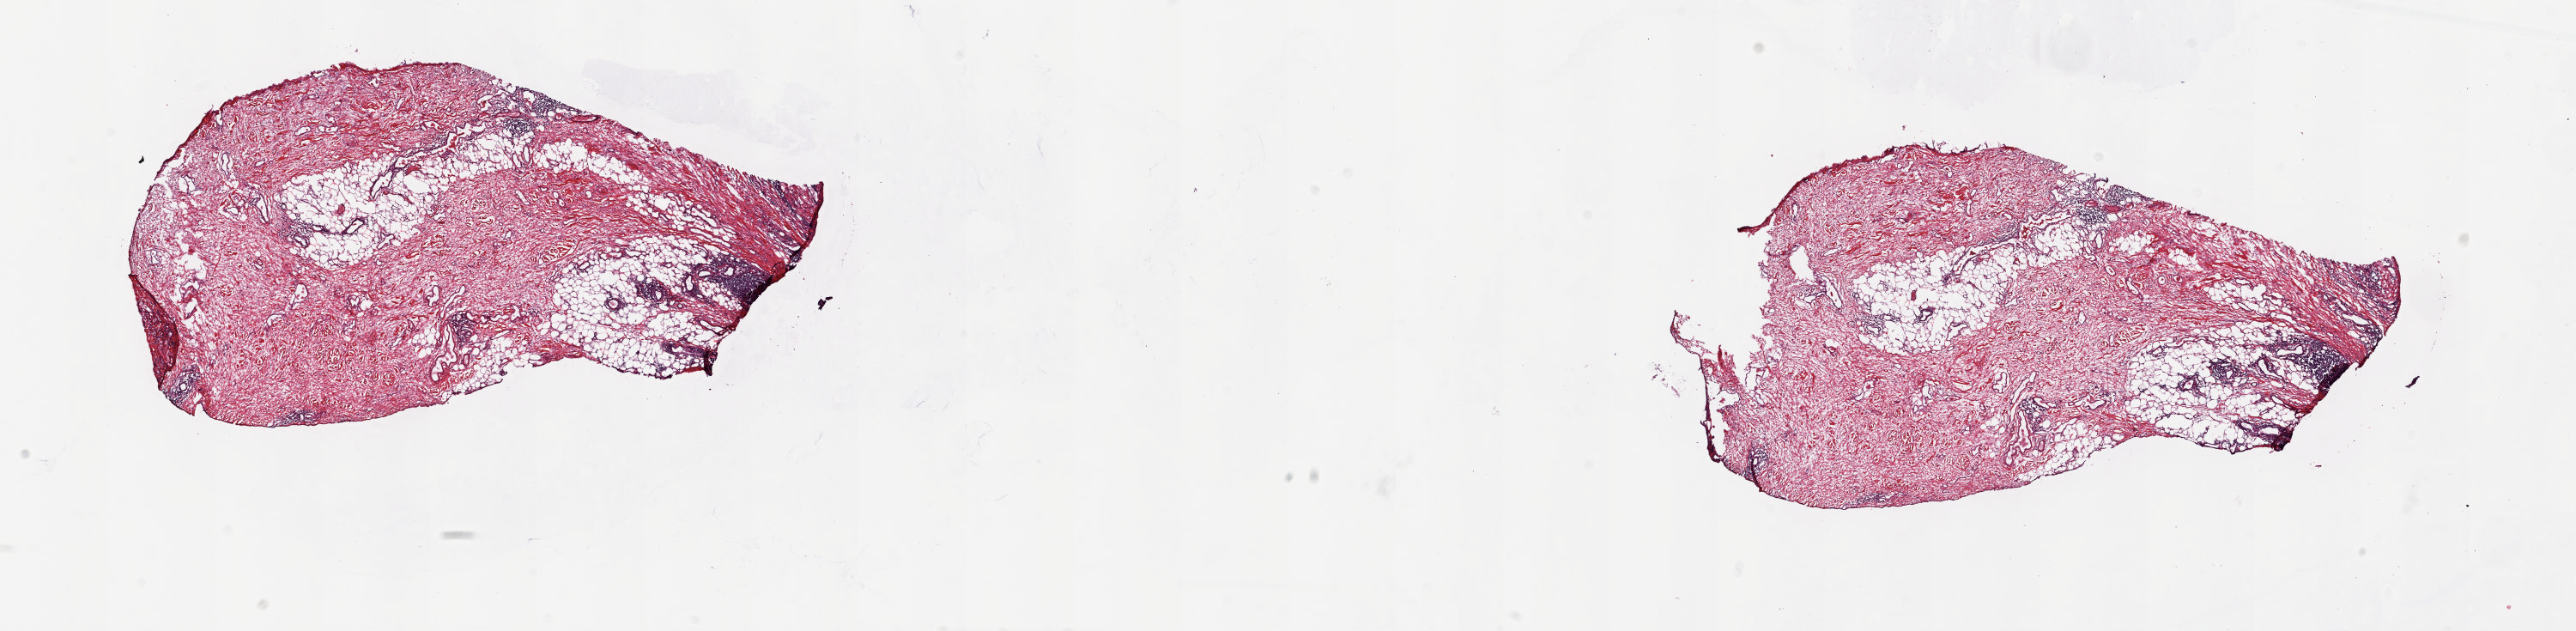
Whole-slide histology image, Hematoxylin and eosin (H&E) stained — shown as a low-resolution overview of the whole scanned area (about 23.8 x 5.8 mm, from a 20x scan); frozen section; skin, solid tissue normal (non-tumour tissue) sample. Male, age 51 years at initial diagnosis. Composition of this section per pathologist review: tumour cells 0%, tumour nuclei 0%, normal cells 100%, stromal cells 0%, necrosis 0%. Inflammatory infiltration, as recorded: lymphocyte infiltration 0%, monocyte infiltration 0%, neutrophil infiltration 0%.
* this section: solid tissue normal sample (biorepository sample class)
* patient diagnosis: Malignant melanoma, NOS